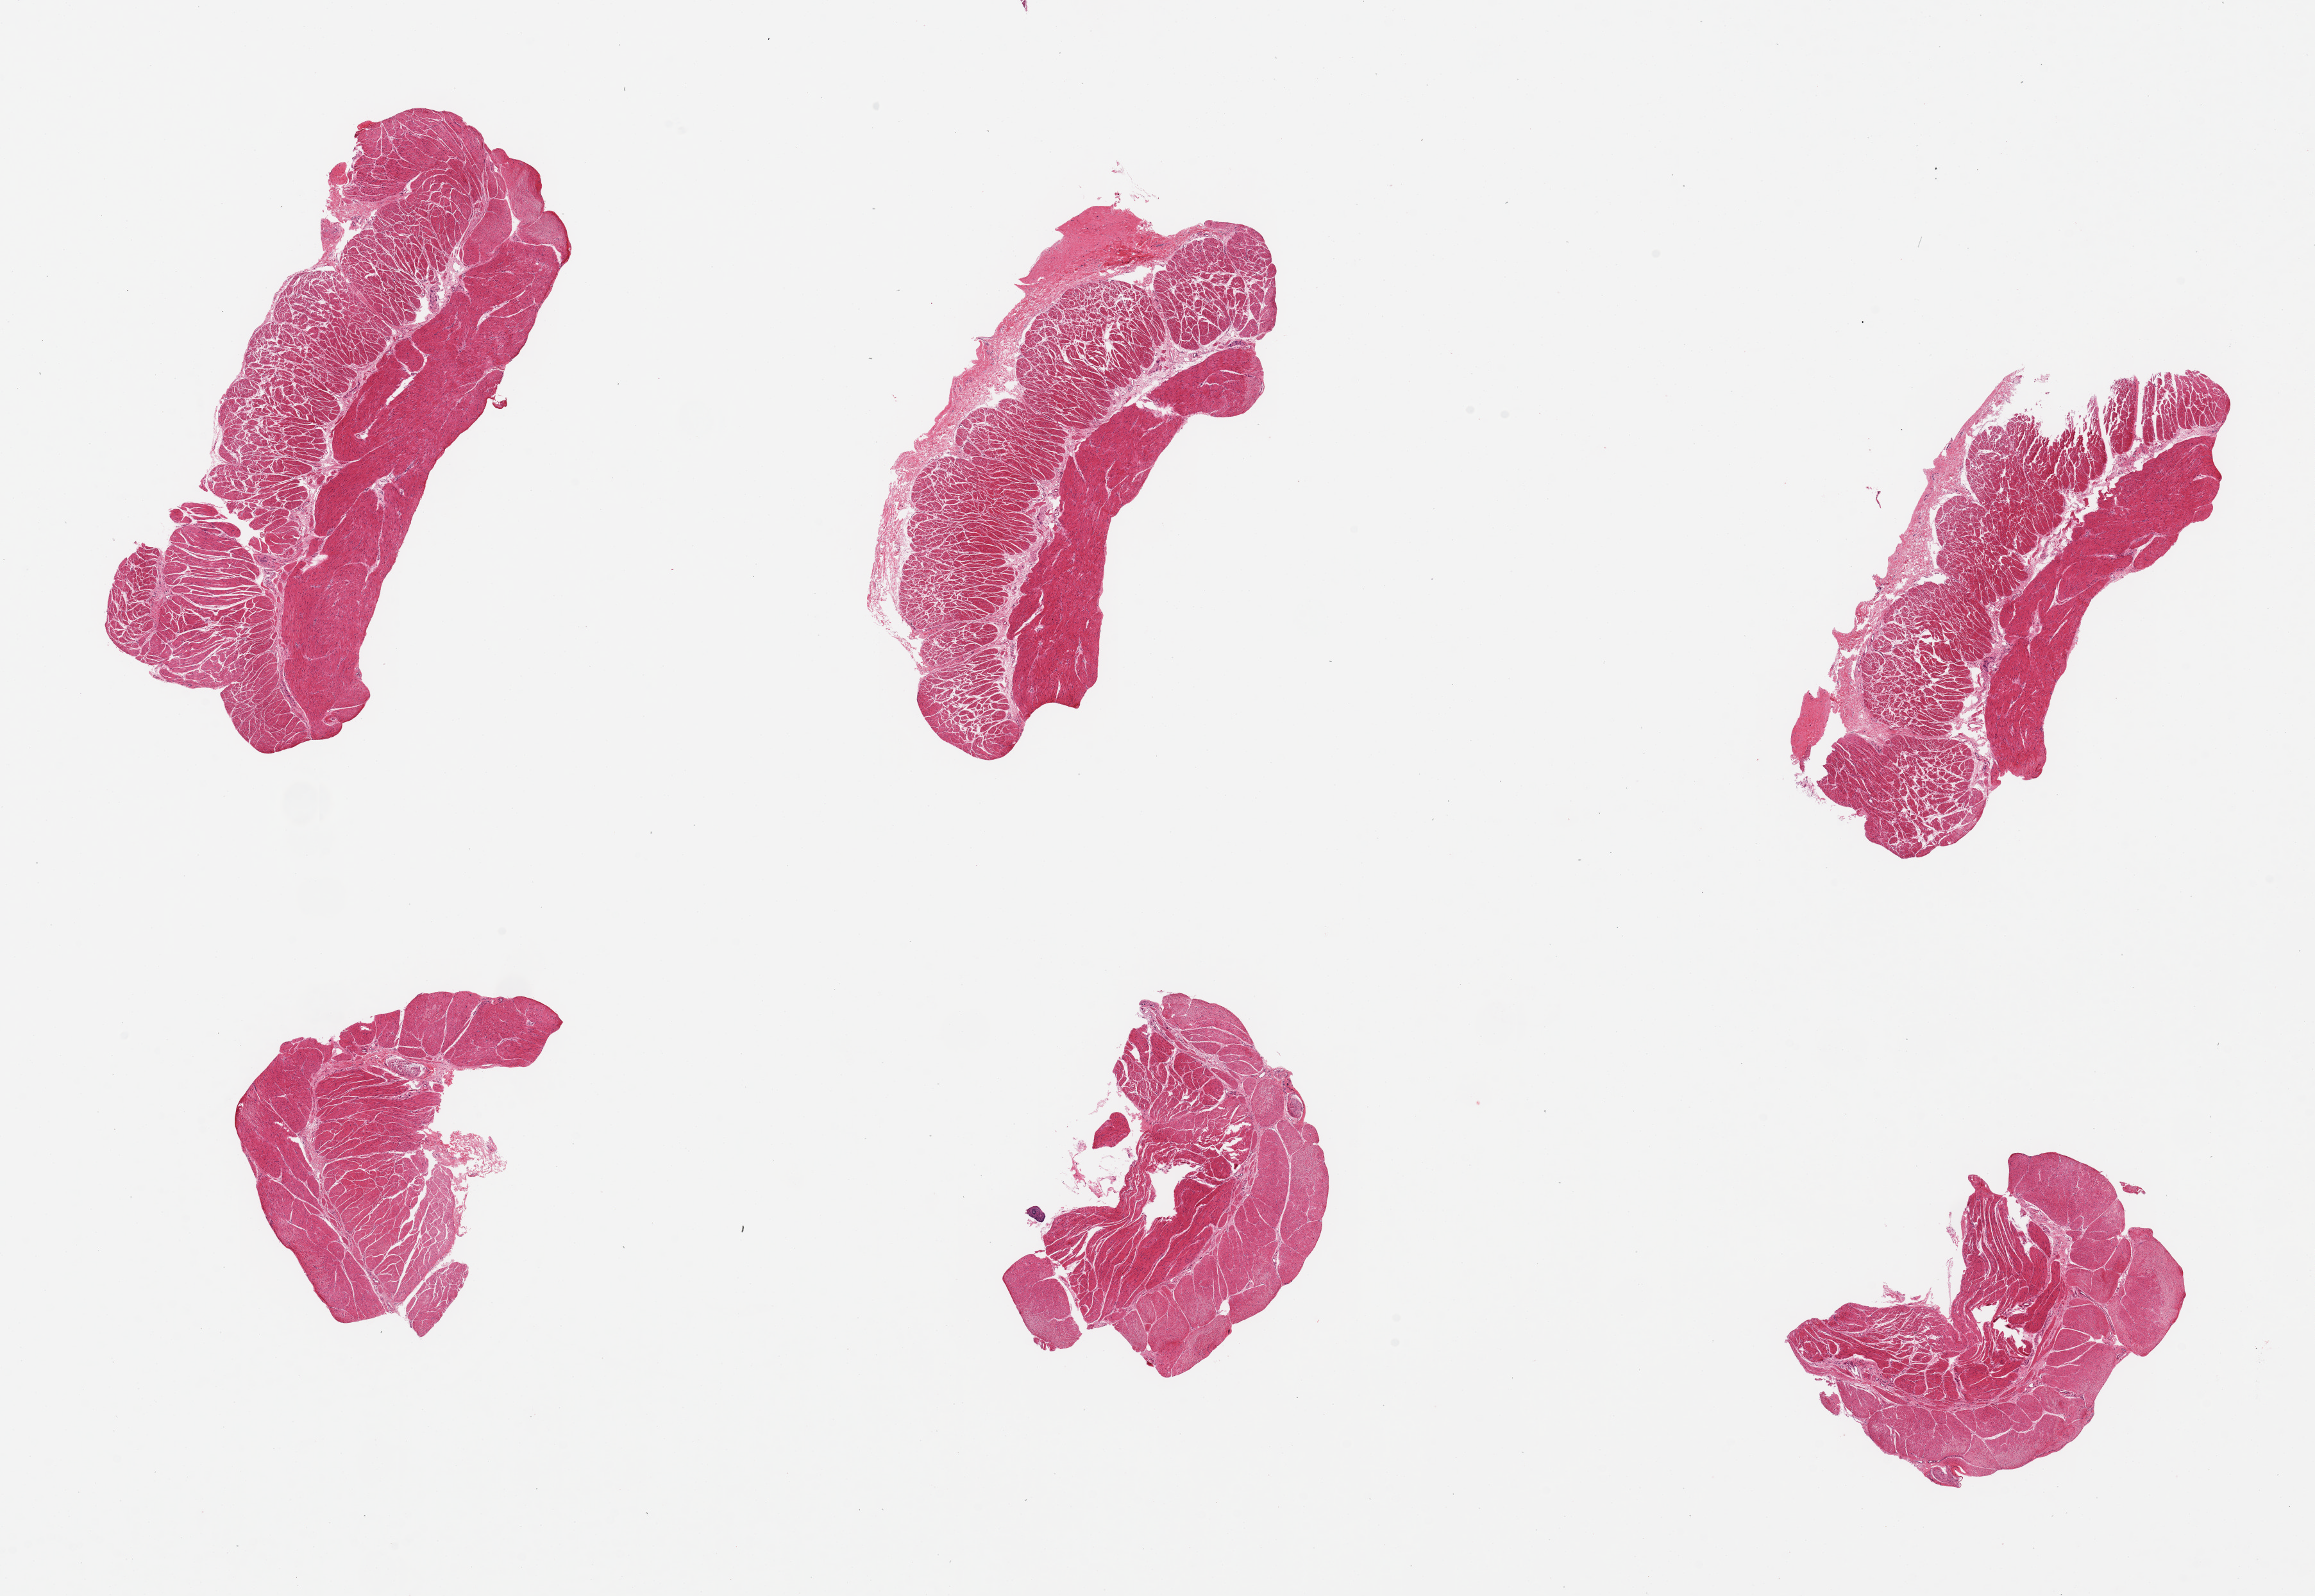
Haematoxylin and eosin whole-slide image, low-resolution overview of the scanned area, about 28.5 x 19.7 mm (acquisition: 20x scan); PAXgene-fixed paraffin-embedded (PFPE) section; sampled site (target tissue): esophageal muscle; tissue donor sample. Donor sex: female.
• pathologist's review note for this sample: 6 pieces, up to 8x4mm; good muscle and neural tissue